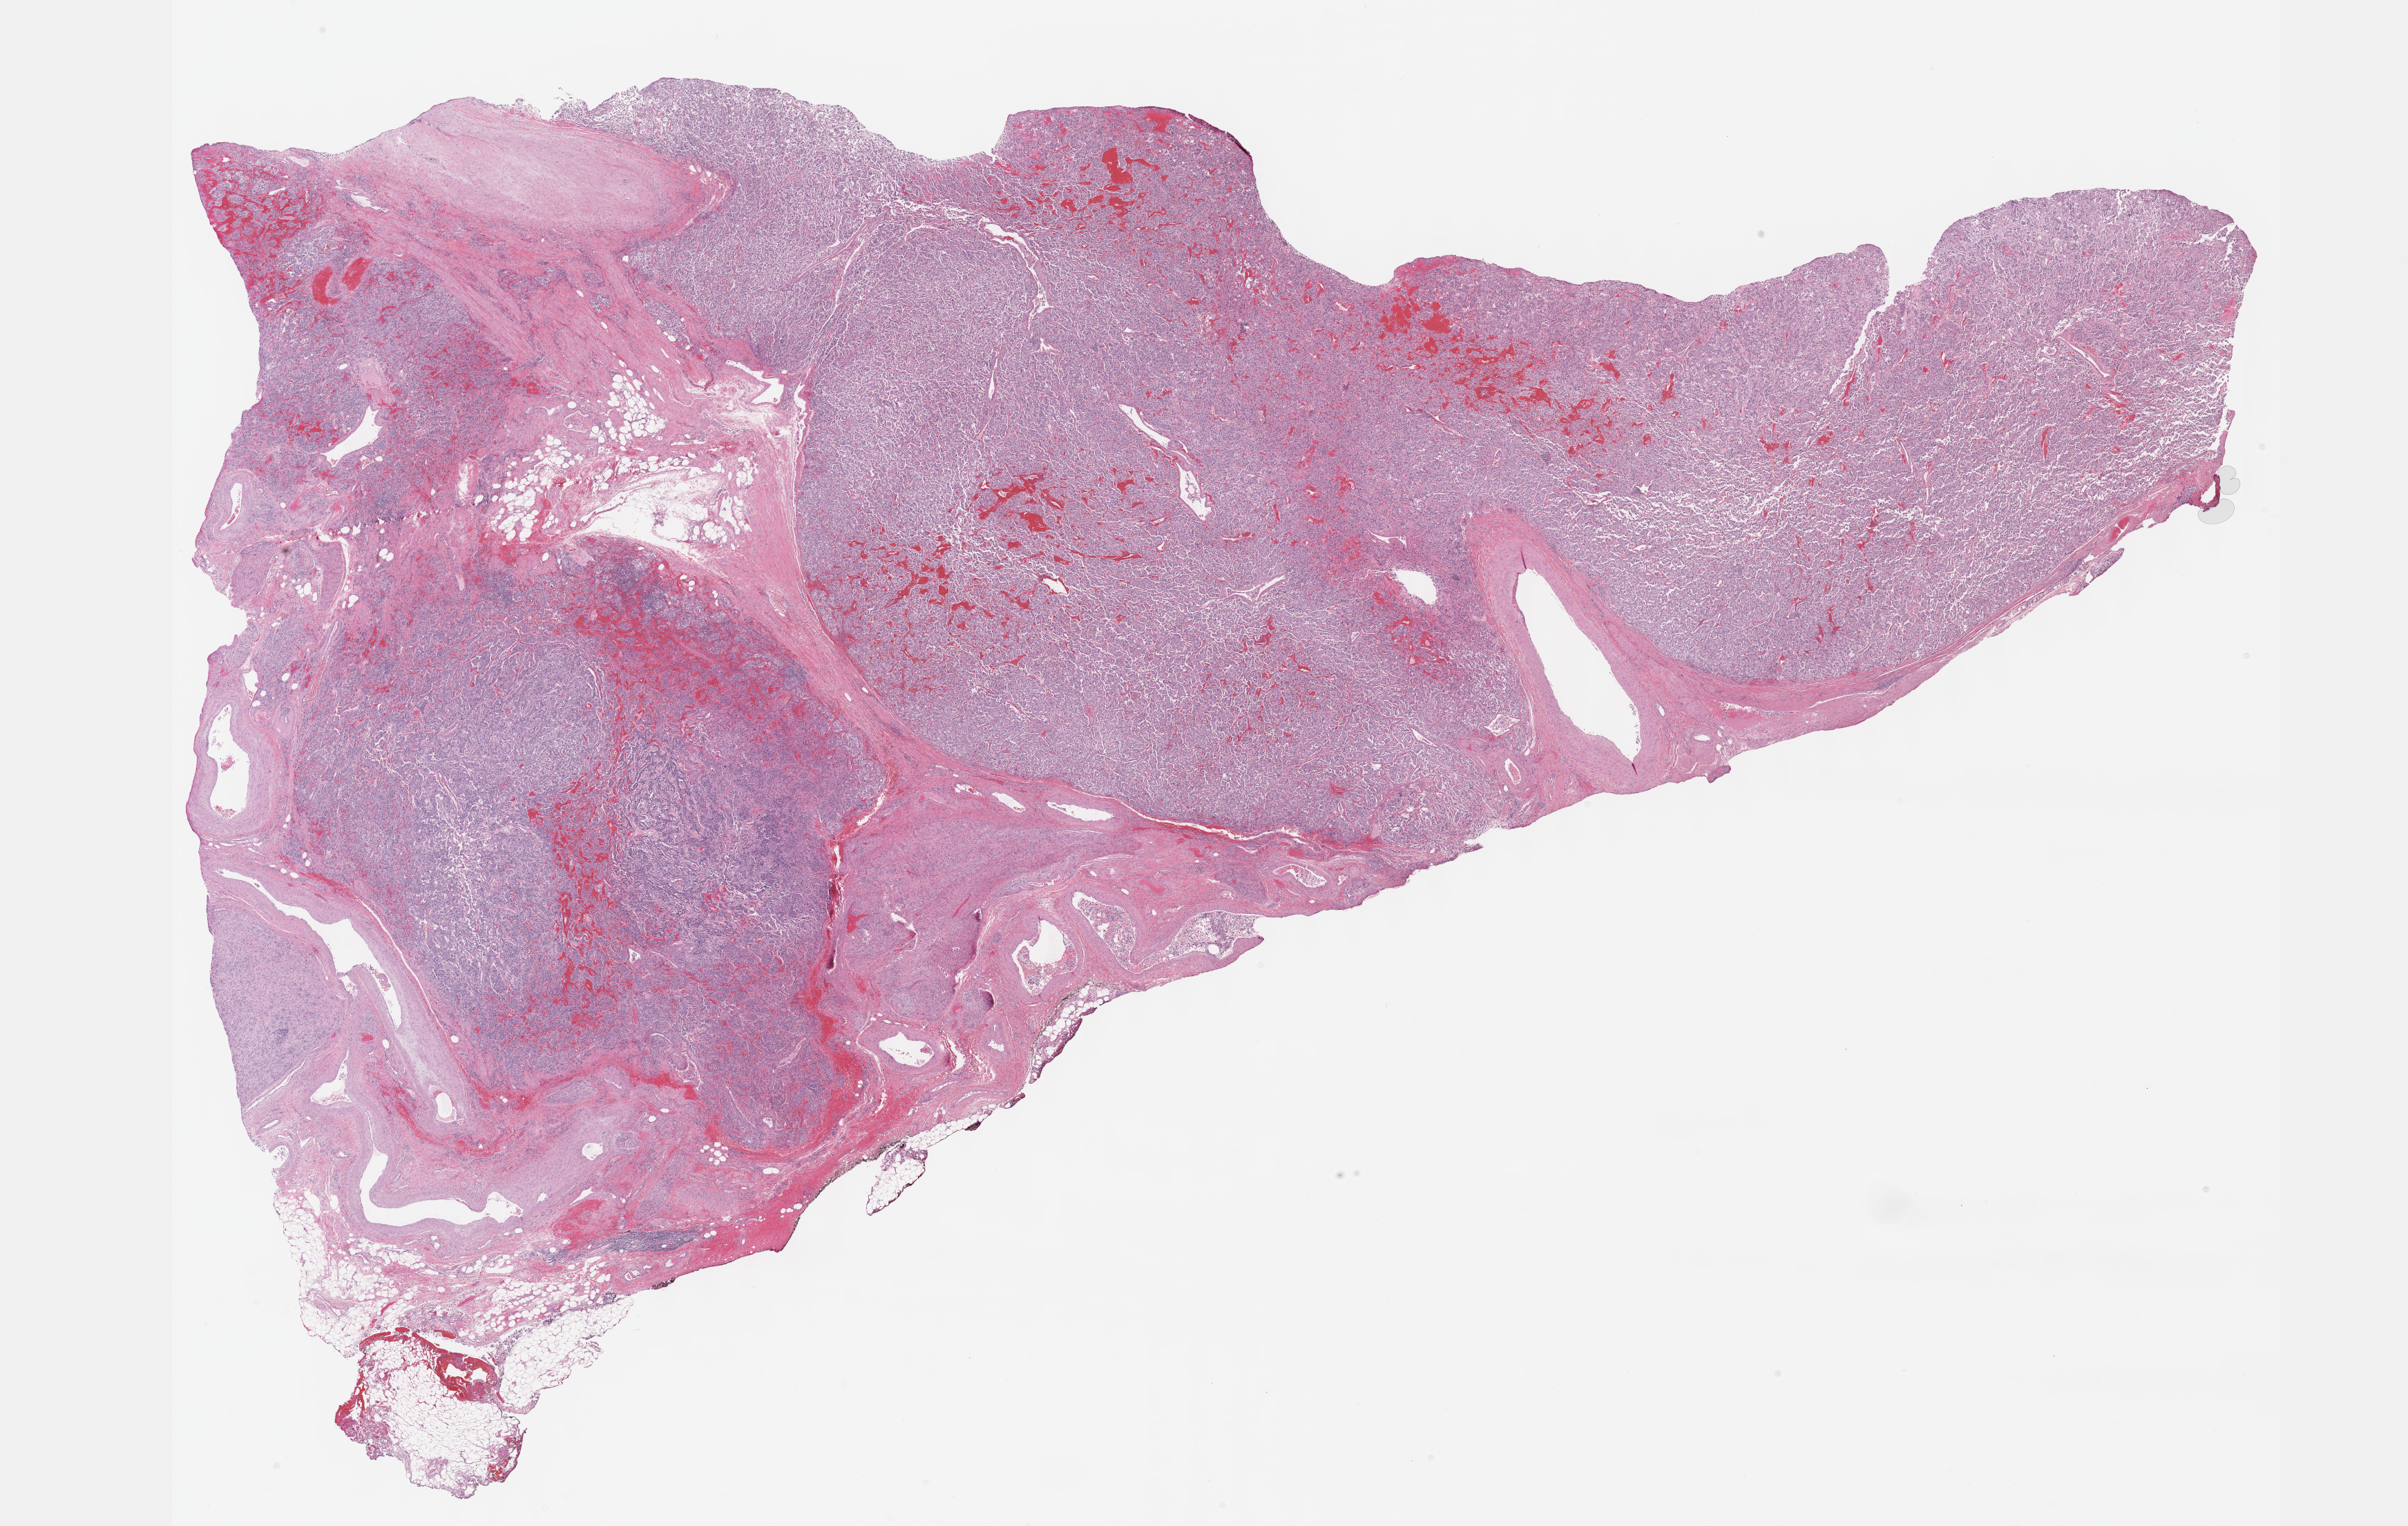
H&E whole-slide image — a low-resolution overview of the entire scanned area, about 28.2 x 17.8 mm; formalin-fixed paraffin-embedded (FFPE) diagnostic section; retroperitoneum and peritoneum, primary tumour sample. Female, age 45 years at initial diagnosis.
• lymph nodes positive (case pathology): 0 of 1 examined
• pathologic diagnosis: Extra-adrenal paraganglioma, NOS (retroperitoneum)